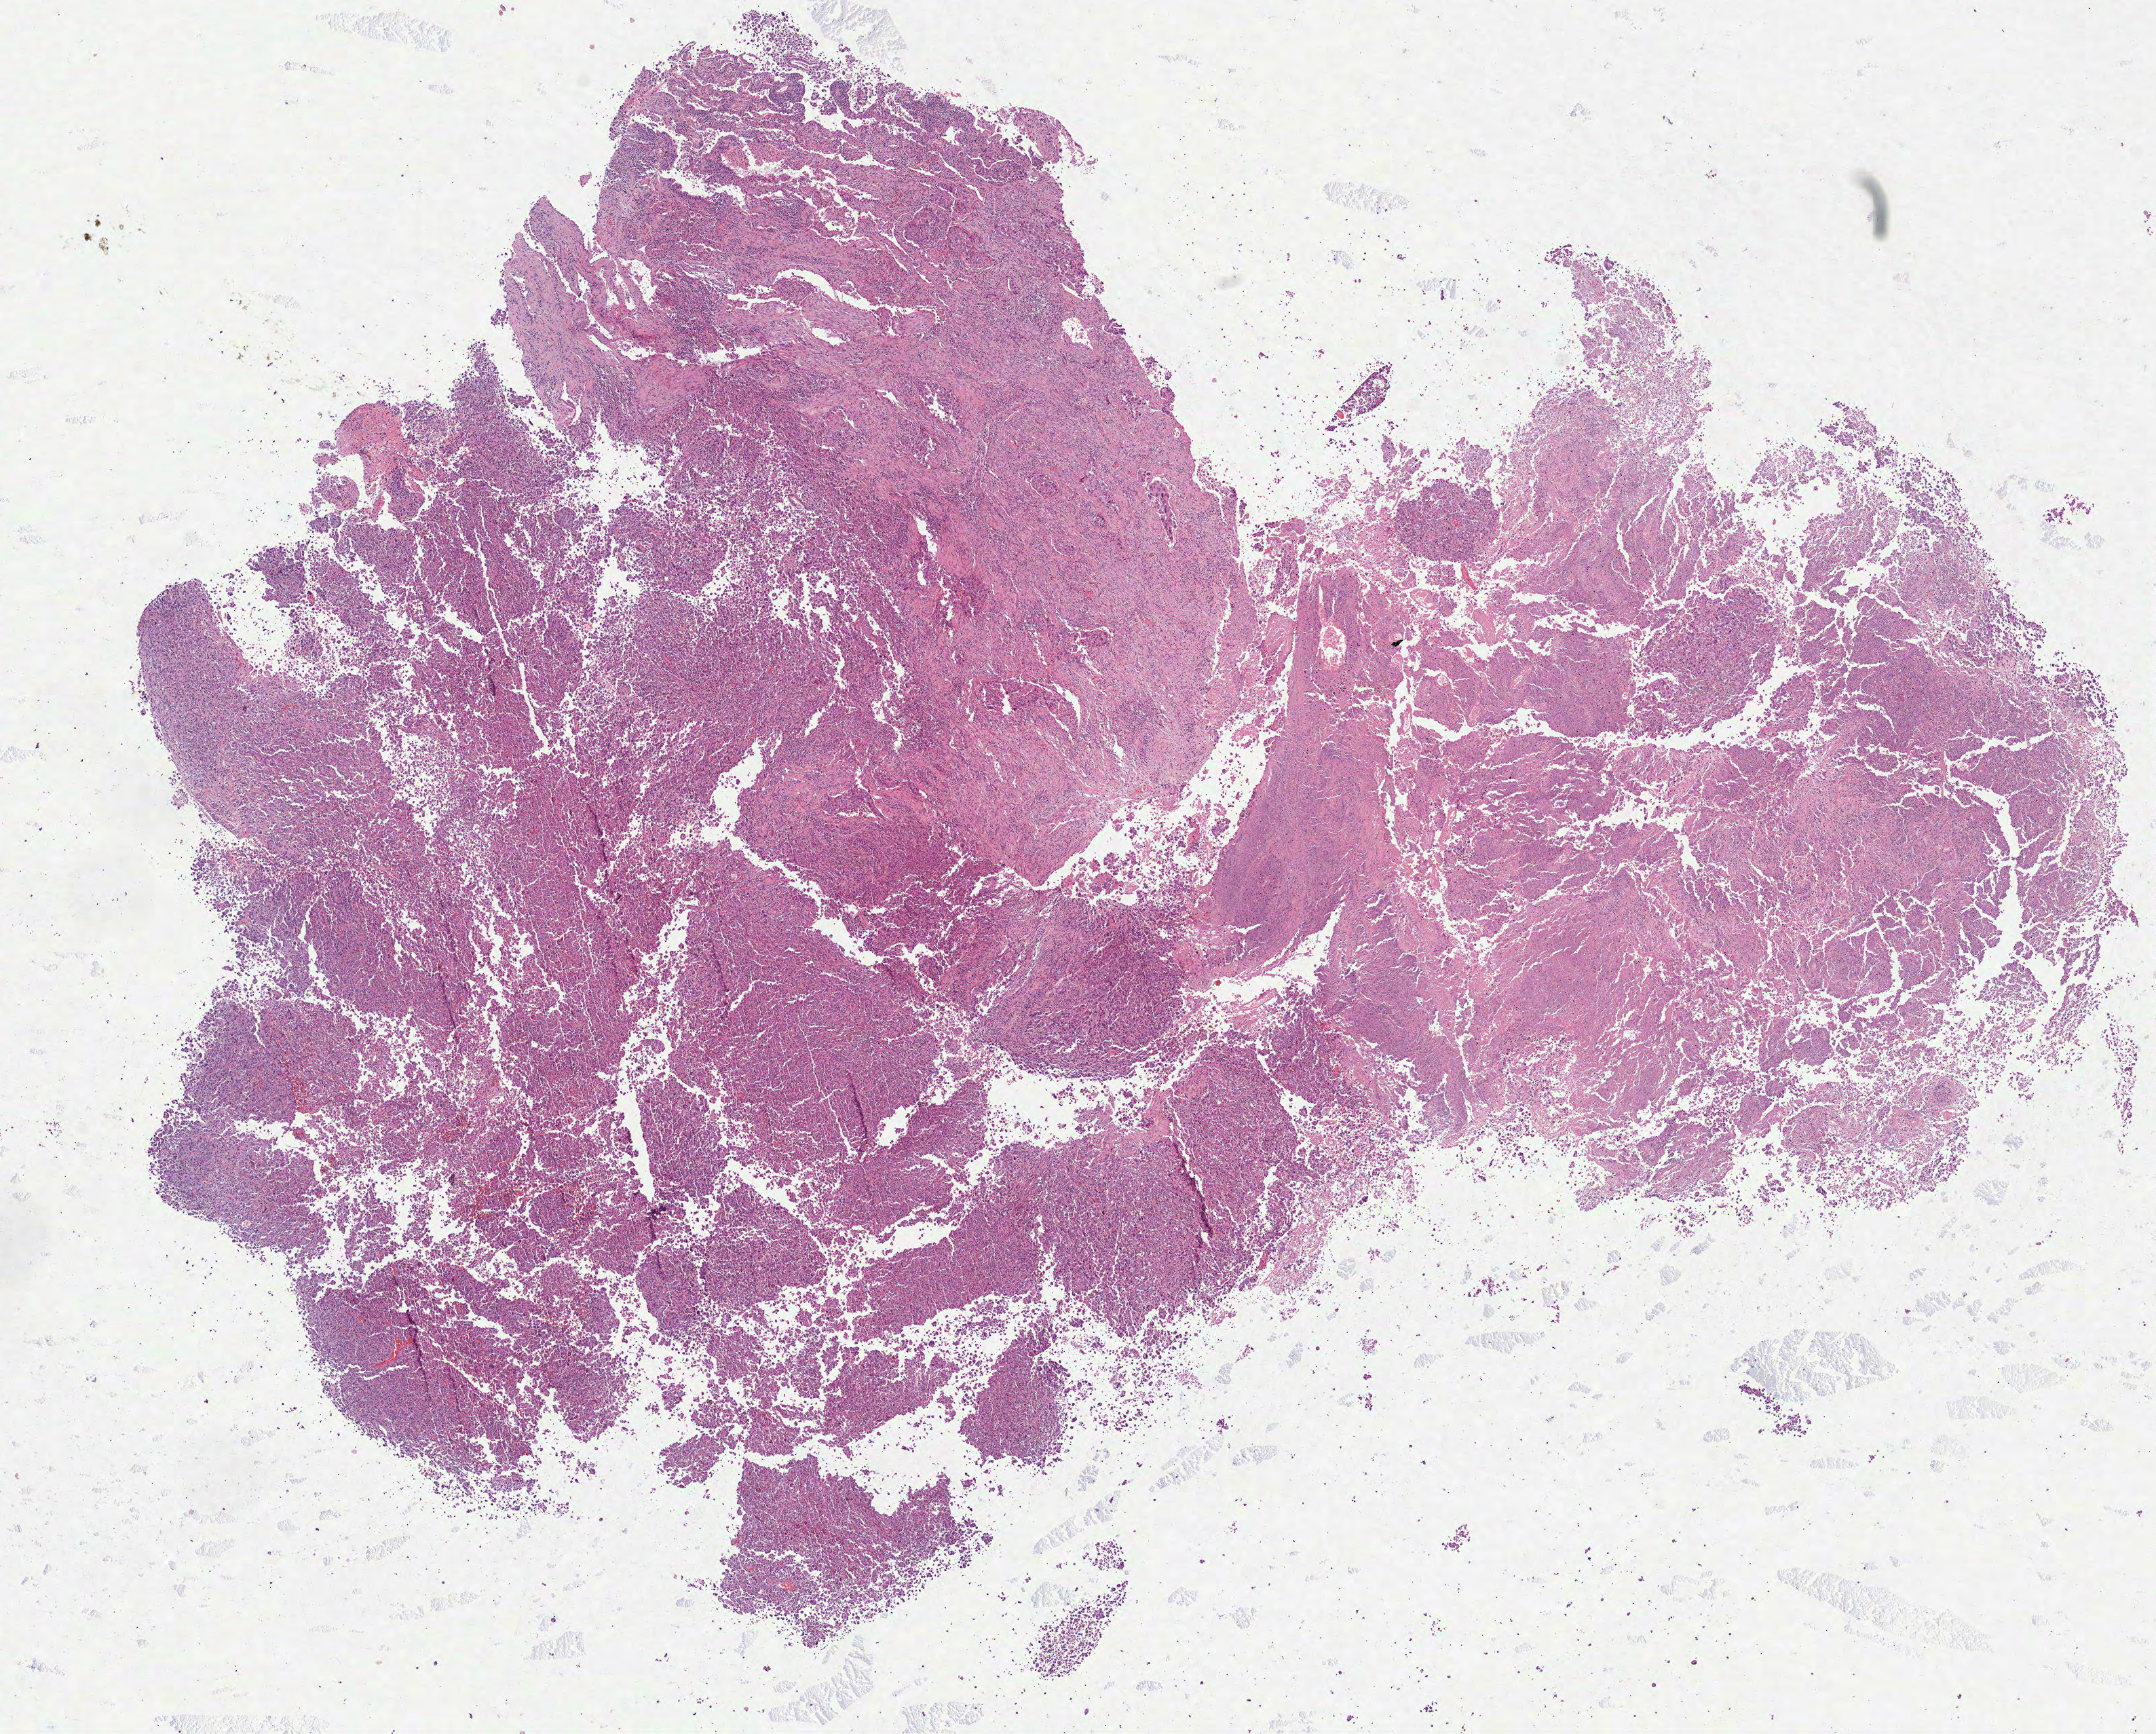
Whole-slide histology image, H&E — shown as a low-resolution overview of the whole scanned area (about 12.8 x 10.3 mm); formalin-fixed paraffin-embedded (FFPE) diagnostic section; sample: primary tumour, lung. Patient: male, age at initial diagnosis 81 years.
Diagnosis: Adenocarcinoma, NOS (middle lobe, lung).